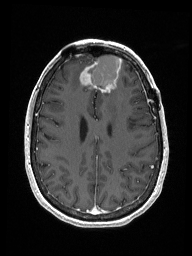
Brain MRI from a brain-tumour surgery series, one axial slice. Slice 60 of 192 in the series (ordered by position). T1-weighted post-contrast. 1 mm slice thickness. 192 × 256 image matrix, field of view 187 × 250 mm. From the clinical record (not read from this slice): histopathology: Metastastic Carcinoma from Breast primary; tumour location: Right Frontal.
Structures marked on this image (outlined manually by an expert reader):
- previous resection cavity: box from (x=88, y=55) to (x=121, y=89) px